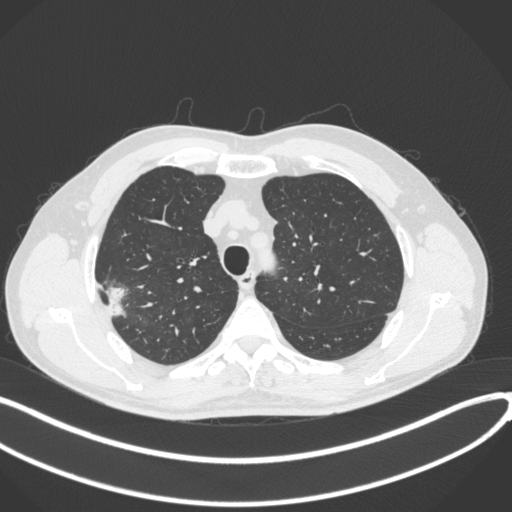
Chest CT, one axial slice. Position 328 of 381 along the scan axis. Lung window (W 1500 / L -600 HU). 1 mm slice thickness. 512 × 512 image matrix, field of view 400 × 400 mm. Male patient, age 62 years. From the clinical record (not read from this slice): clinical TNM (as recorded): T1c N0 M0; histopathological grade: G2-3.
Annotated regions visible in this slice (rectangle marked by the reading radiologist):
- lung tumour (recorded histology: adenocarcinoma): bounding box [x1, y1, x2, y2] px = [103, 282, 130, 320]